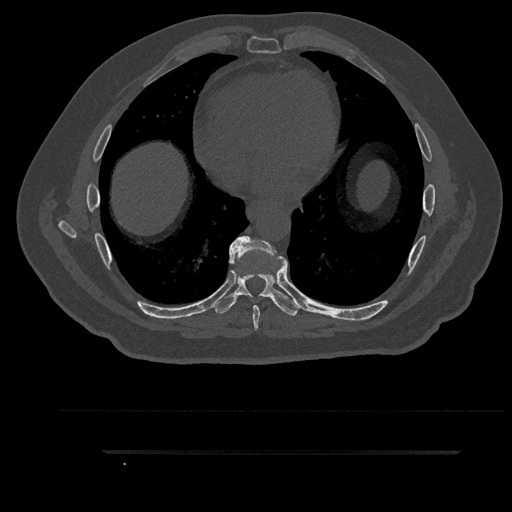
CT including the spine, one axial slice. Reconstruction kernel Br40s/3. Bone window (W 1800 / L 400 HU). 0.5 mm slice thickness. 512 × 512 image matrix, field of view 432 × 432 mm. Patient: male, 63 years. From the clinical record (not read from this slice): primary cancer: renal; vertebrae with lytic lesions (as recorded): T8.
Structures marked on this image (semi-automatic segmentation, software-assisted and operator-edited):
- T6 vertebra: bounding box (x1, y1, x2, y2) in pixels: (251, 295, 253, 297)
- T7 vertebra: (229, 236, 287, 331)
- T8 vertebra: (212, 247, 301, 316)